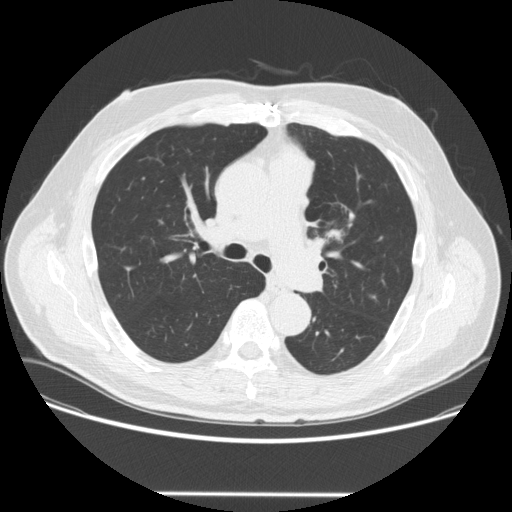
Low-dose screening chest CT, one axial slice; slice 166 of 253 in the series (ordered by position); lung window (W 1500 / L -600 HU); 2.5 mm slice thickness; 512 × 512 image matrix, field of view 400 × 400 mm.
Structures marked on this image (manually delineated by an expert):
- lesion 1 (tumor, upper lobe of left lung): bounding box [x1, y1, x2, y2] px = [329, 230, 341, 238]